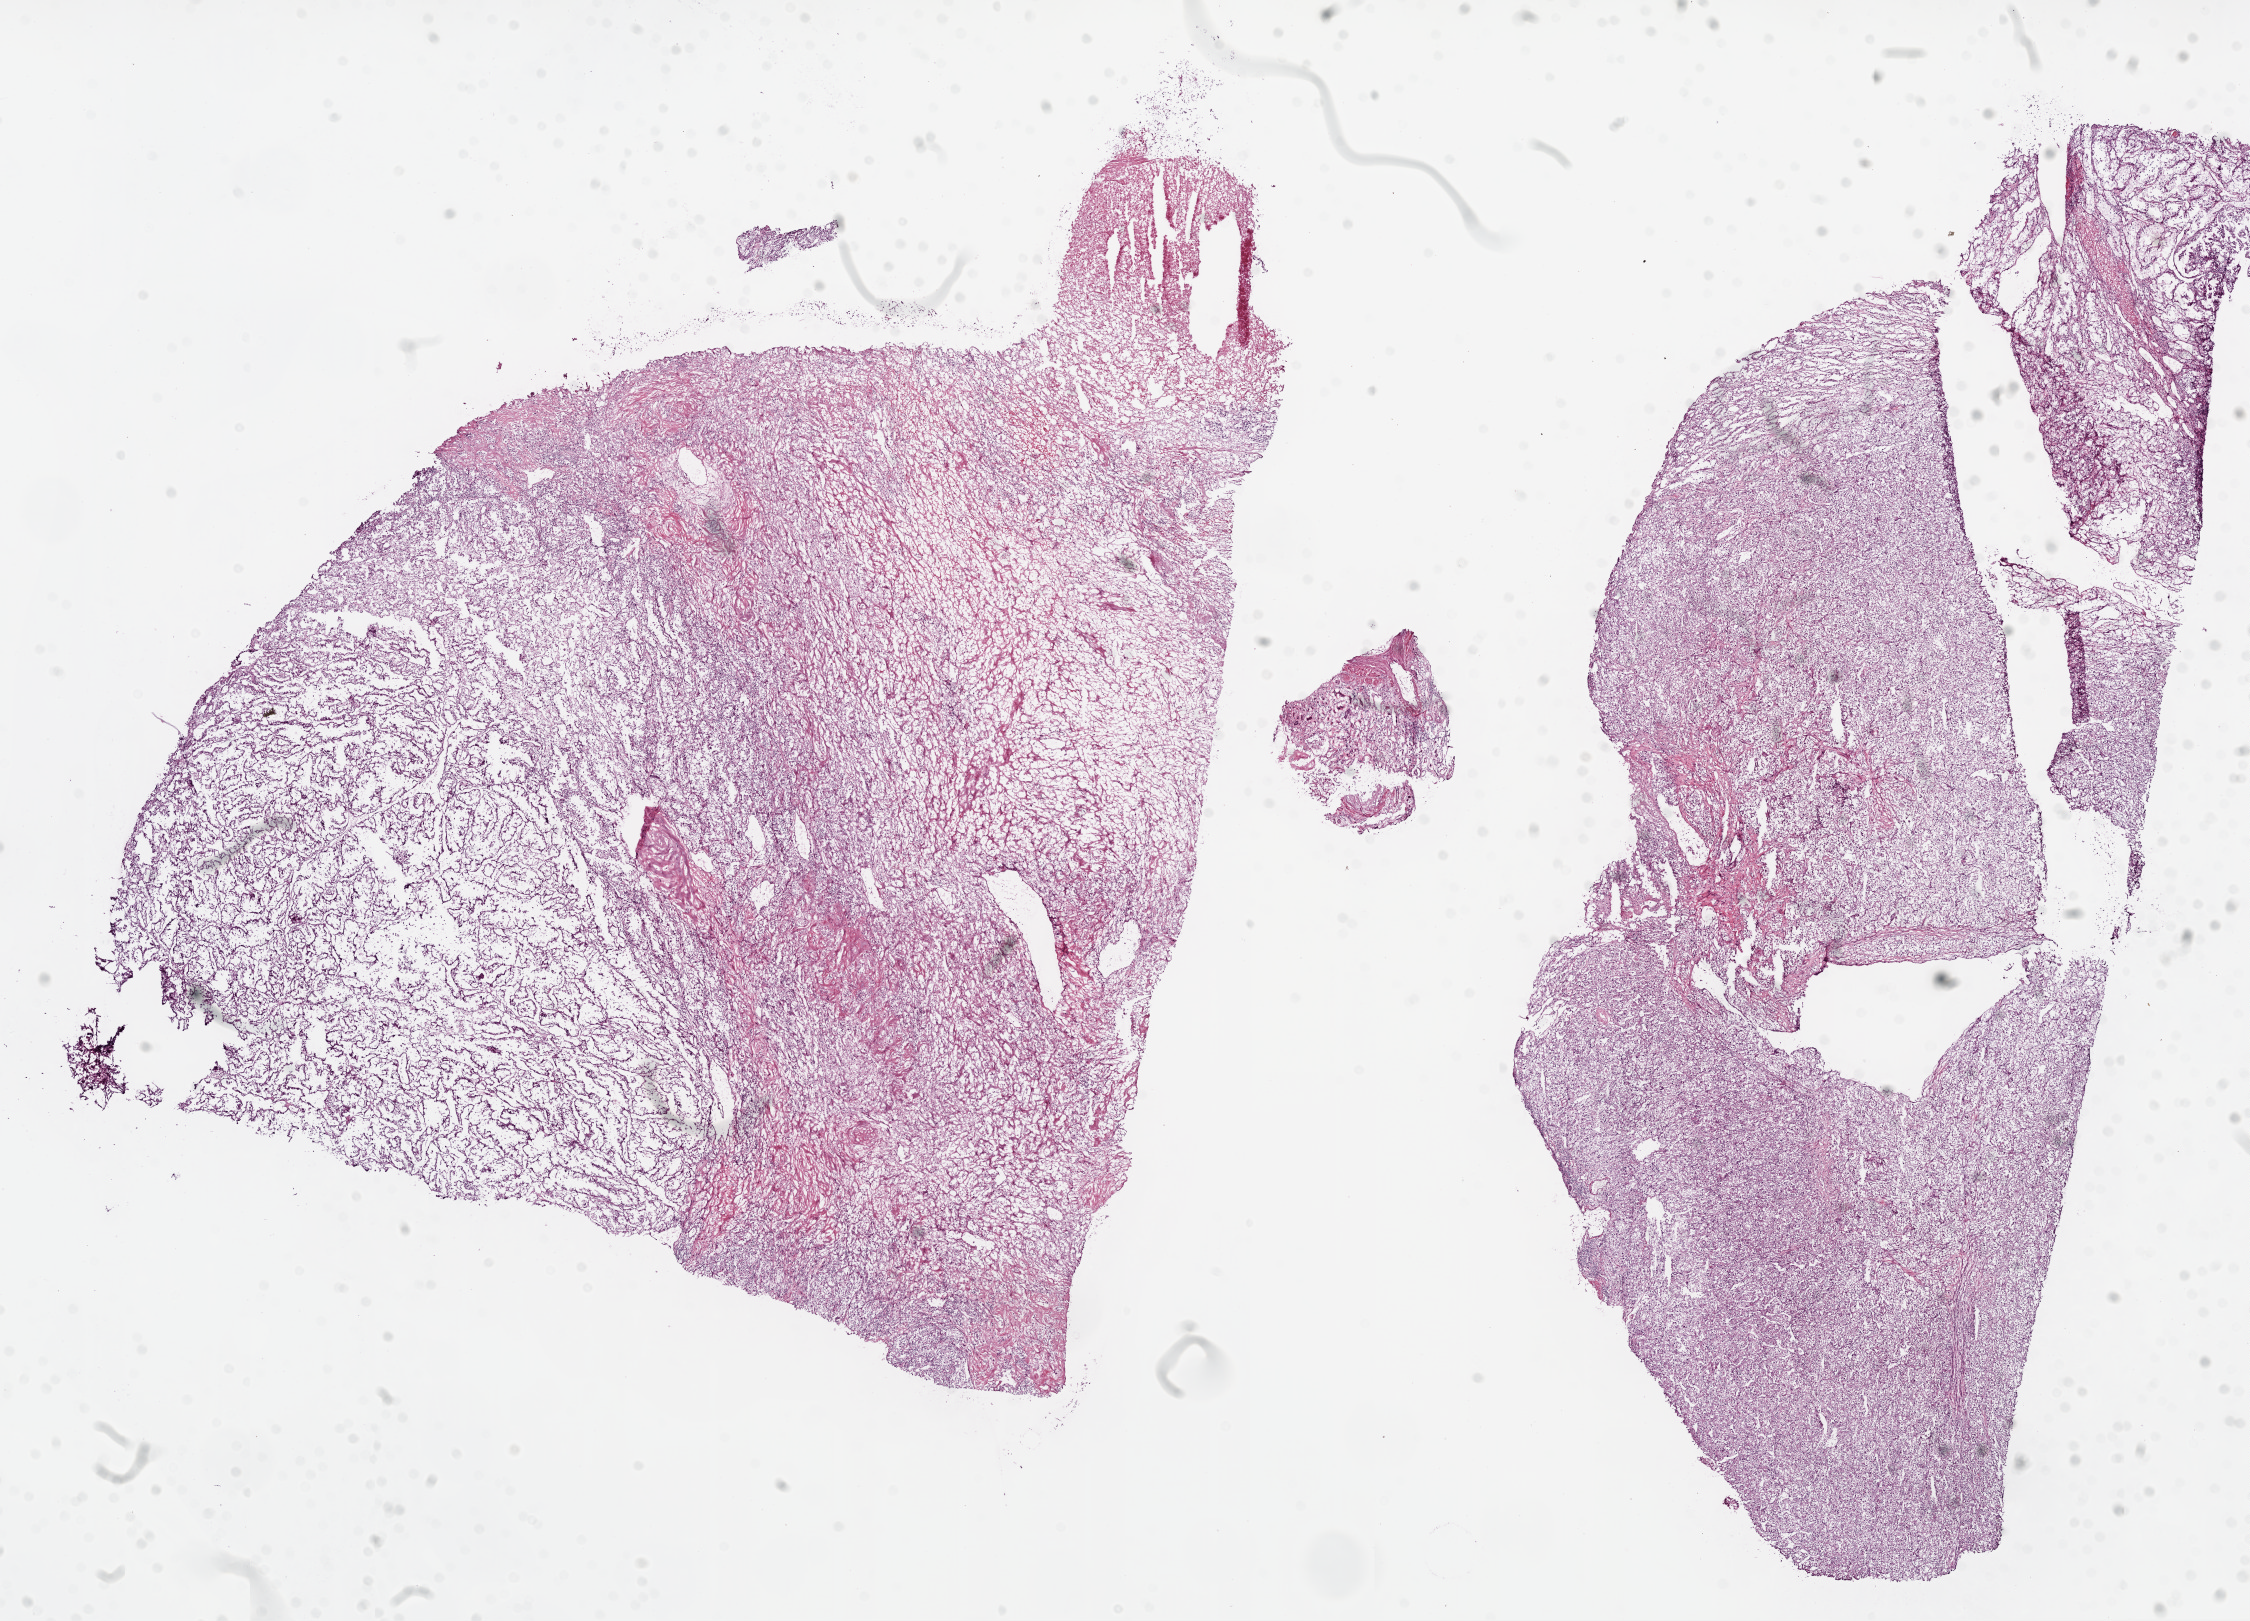
Whole-slide histology image, Hematoxylin and eosin (H&E) stained, shown as a low-resolution overview of the whole scanned area (about 18.1 x 13.0 mm, slide scanned at 20x). Frozen section. Sample: primary tumour, kidney. Patient: male, age at initial diagnosis 72 years. Histologic grade: G4 (undifferentiated). Composition of this section per pathologist review: tumour cells 85%, tumour nuclei 85%, normal cells 0%, stromal cells 10%, necrosis 5%.
AJCC pathologic stage: III. Diagnosis: Clear cell adenocarcinoma, NOS.